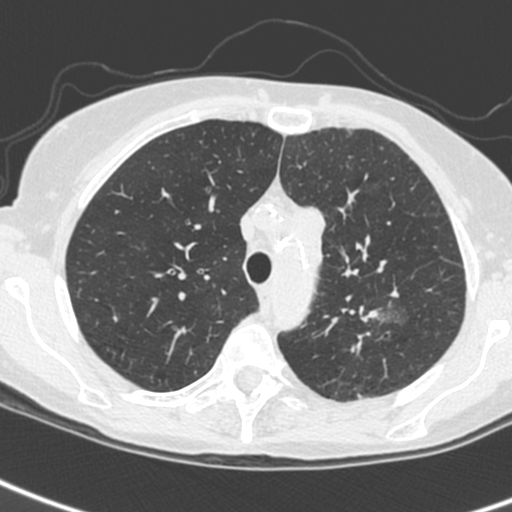
Chest CT (low-dose screening protocol), one axial image, baseline screening round, lung window (W 1500 / L -600 HU), standard (soft-tissue) reconstruction kernel (C). Female participant, aged 61 years at enrolment.
Expert reader's lesion annotation, box from (x=343, y=289) to (x=411, y=346) px. The screening reader recorded 2 non-calcified nodules or masses ≥4 mm on this exam (left upper lobe, left upper lobe); which of them this box marks is not recorded. Lung cancer was diagnosed 29 days after this screen: small cell carcinoma, NOS, left upper lobe, stage IV (AJCC 6th edition).